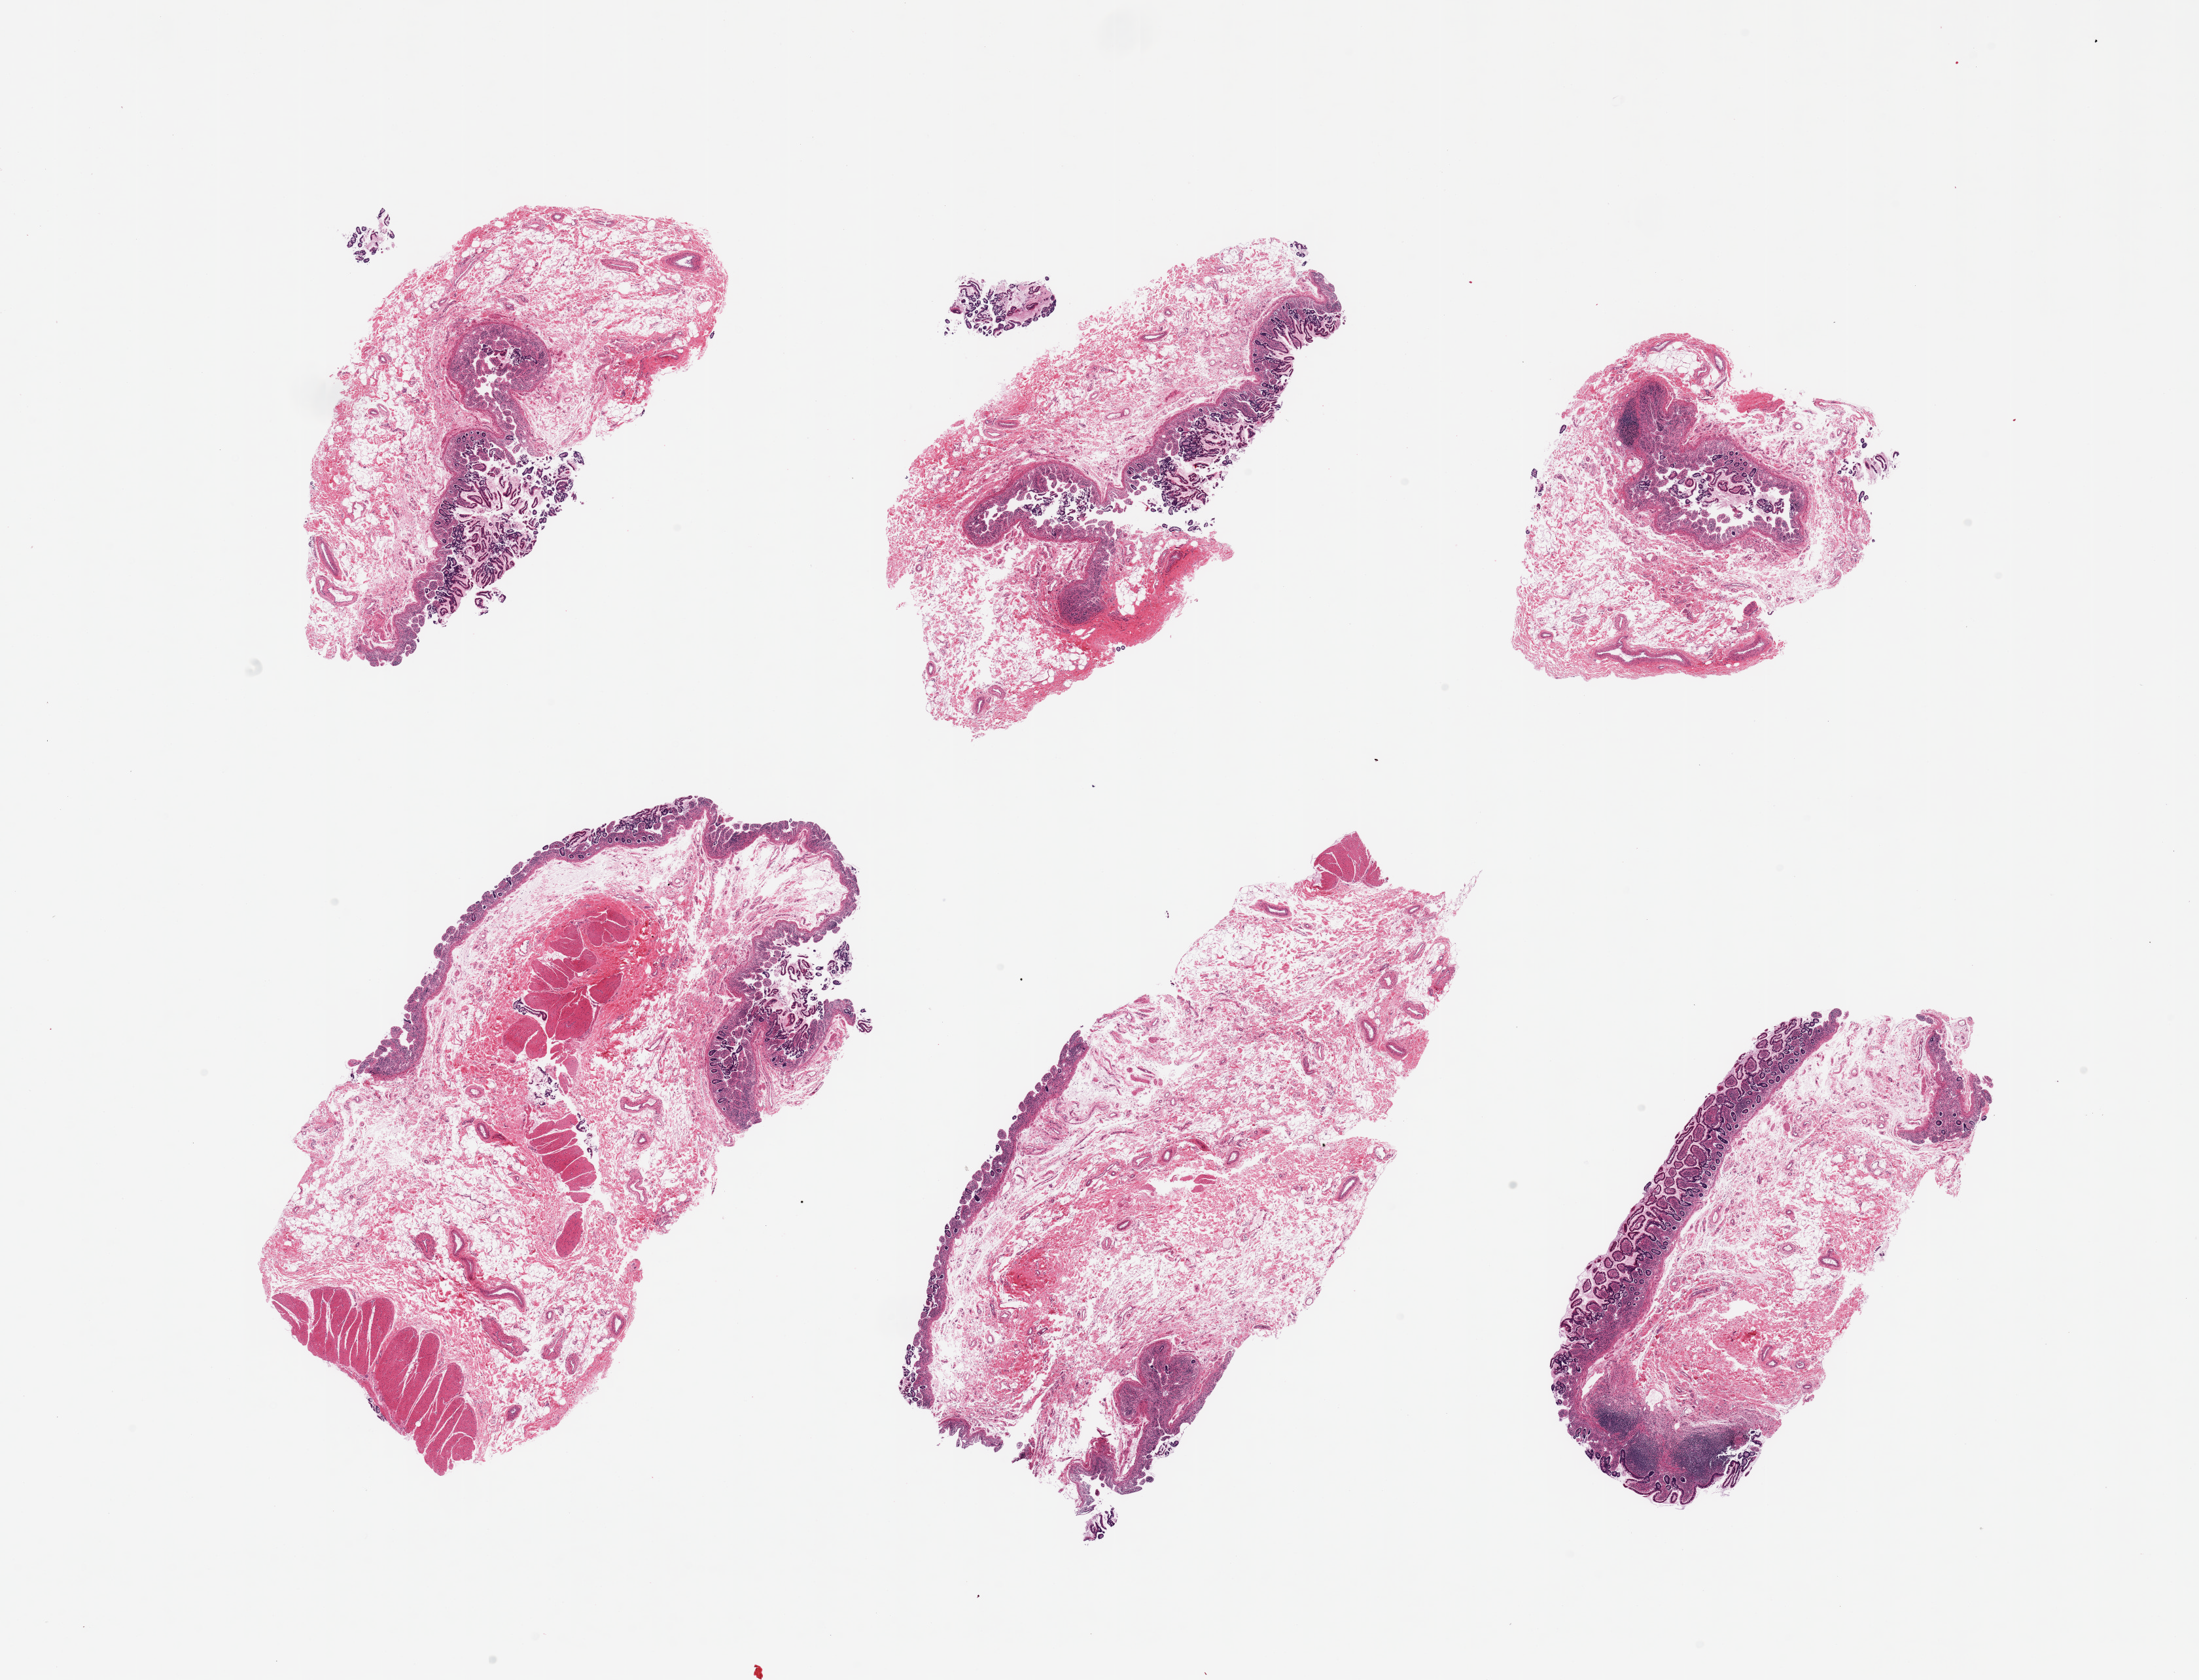
Digitized H&E-stained section — a low-resolution overview of the entire scanned area, about 26.6 x 20.3 mm. PAXgene-fixed, paraffin-embedded tissue. Section of ileum (target tissue). Donor tissue sample. Male donor.
Reviewer comment on this tissue sample: 6 pieces; moderately to severely autolyzed mucosa and residual target lymphoid aggregates are about 5-10% of tissue.